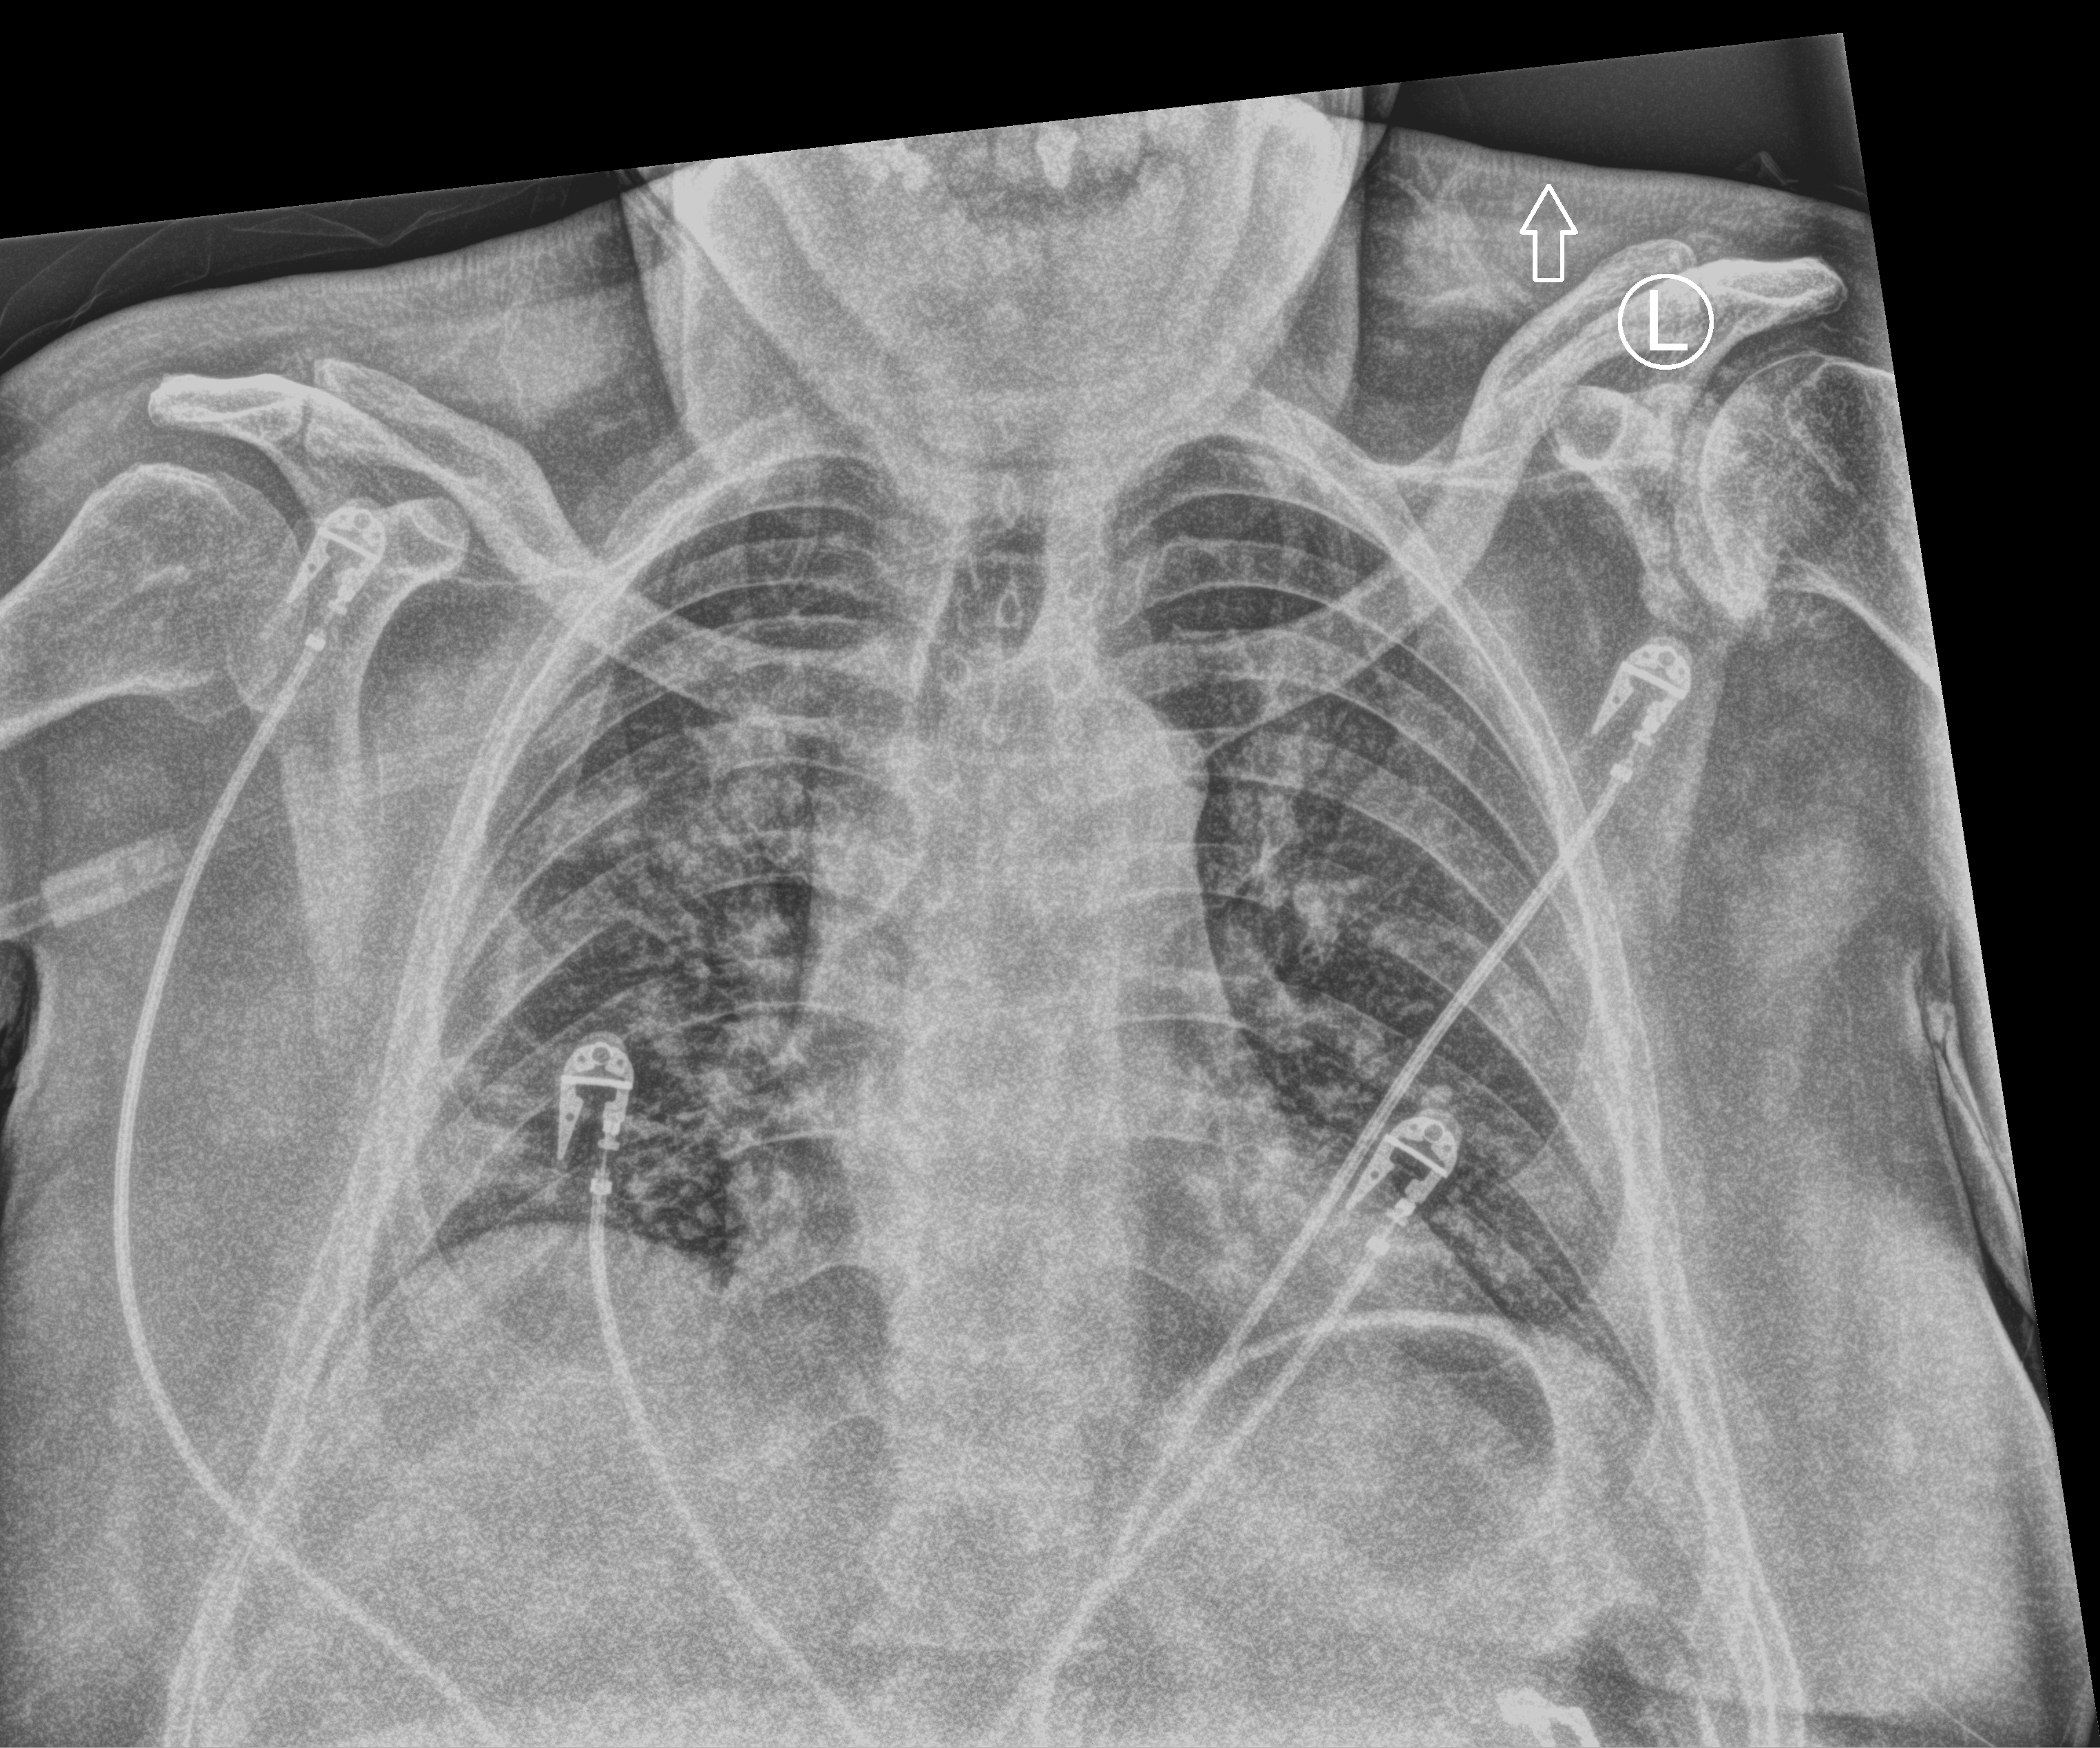
Bedside chest radiograph (computed radiography); anteroposterior (AP) projection. Male patient hospitalised with COVID-19, age 60–74 years.
Admission-level facts for this patient (not findings on this image; timing relative to this image not recorded):
- mechanically ventilated during this hospital stay: no
- admitted to intensive care during this hospital stay: yes
- hypertension (admission record): no